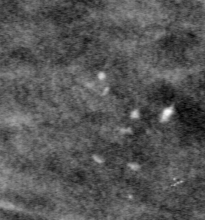
Region of interest cut from a scanned film mammogram (one marked finding), right breast, MLO view, BI-RADS breast density category 4 (scale 1–4).
- Finding: calcifications, morphology pleomorphic, distribution clustered; BI-RADS assessment category 4; pathology result (as recorded, not read from the image): malignant.